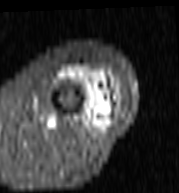
MRI of an extremity soft-tissue mass, one axial slice; position 35 of 103 along the scan axis; STIR; MR volume resampled by the dataset authors to the PET/CT grid (not the native acquisition matrix); 179 × 193 image matrix, field of view 175 × 188 mm. Female patient. From the clinical record (not read from this slice): histological type: undifferentiated – high grade; grade: high; site of the primary tumour: left thigh.
Outlined on this slice (expert contour drawn on MRI and transferred to this co-registered scan by the dataset authors):
- gross tumour volume including surrounding oedema: box from (x=61, y=66) to (x=121, y=127) px